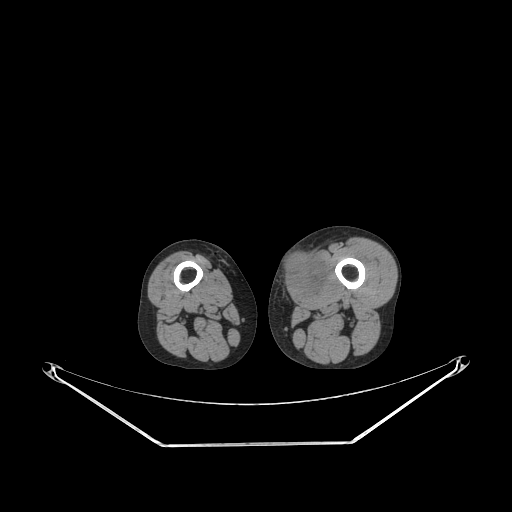
CT of an extremity soft-tissue mass (from a PET/CT study), one axial slice. Position 212 of 267 along the scan axis. Reconstruction kernel STANDARD. 140 kVp. Soft-tissue window (W 400 / L 40 HU). 3.75 mm slice thickness. 512 × 512 image matrix. Male patient. Case-level facts recorded for this patient, not image findings: histological type: pleiomorphic leiomyosarcoma; grade: high; site of the primary tumour: left thigh.
Annotated regions visible in this slice (expert contour drawn on MRI and transferred to this co-registered scan by the dataset authors):
- gross tumour volume including surrounding oedema: bounding box (x1, y1, x2, y2) in pixels: (283, 251, 328, 300)
- gross tumour volume (mass): (283, 253, 325, 296)